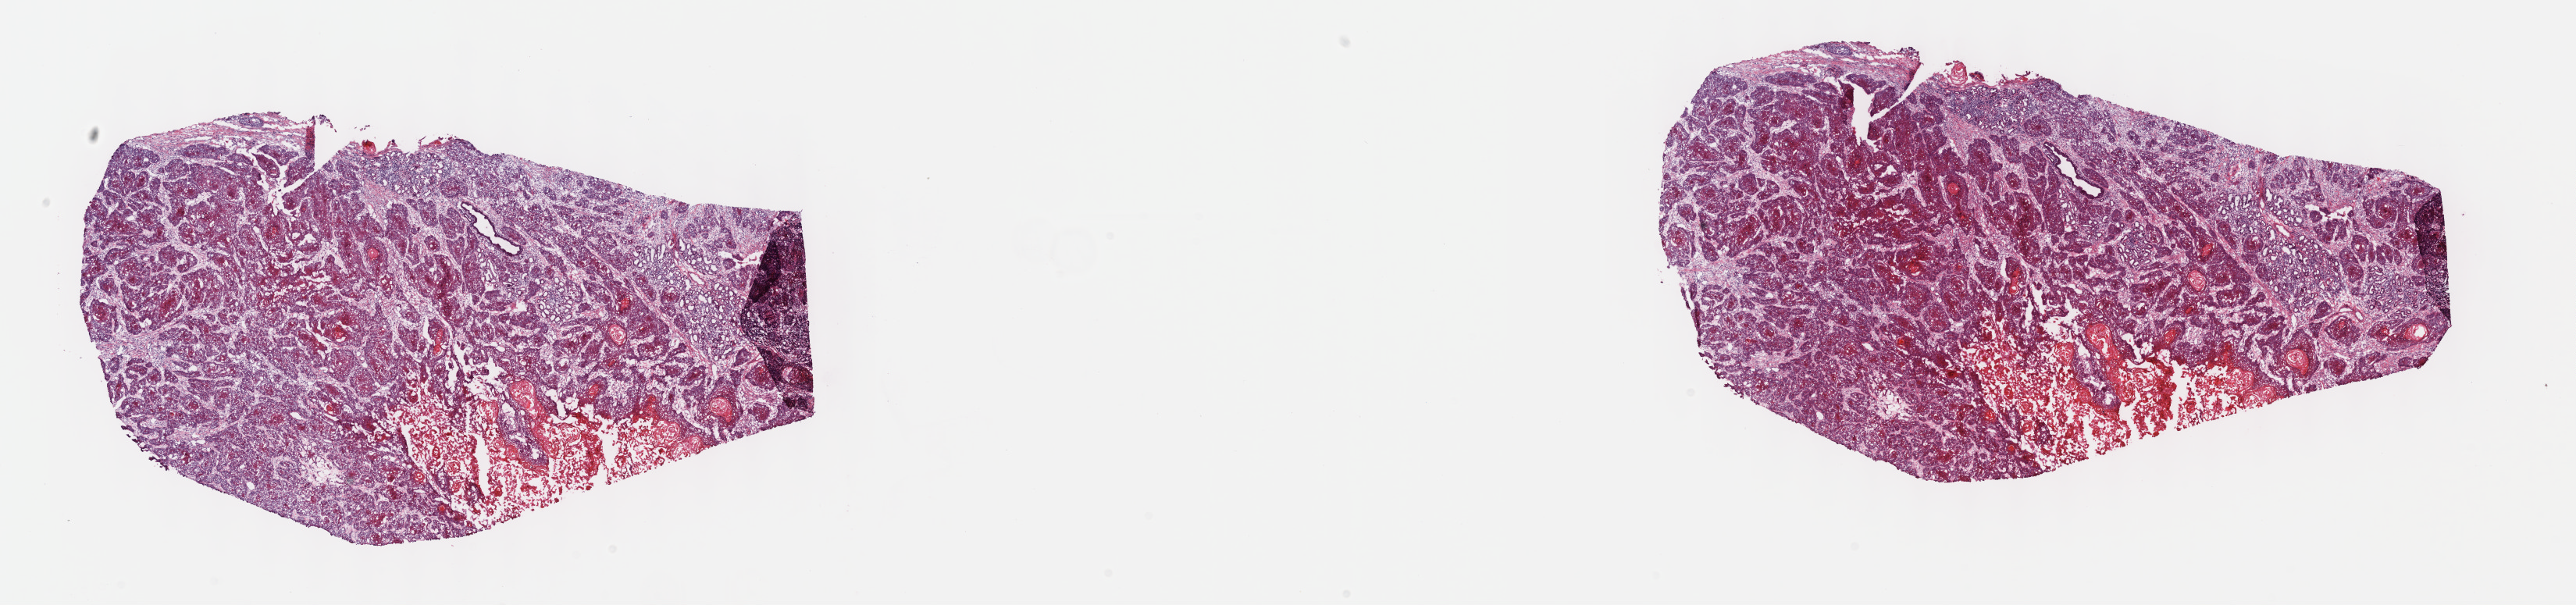
Whole-slide histology image, Hematoxylin and eosin (H&E) stained, whole scanned area (about 26.7 x 6.3 mm) shown as a low-resolution overview, frozen section from the top of the tissue portion, sample: primary tumour, head and neck. Male, age 59 years at initial diagnosis. Histologic grade: G2 (moderately differentiated). Slide review estimates, as recorded: tumour cells 70%, tumour nuclei 80%, normal cells 10%, stromal cells 20%, necrosis 0%. Inflammatory infiltration, as recorded: lymphocyte infiltration 4%, monocyte infiltration 4%, neutrophil infiltration 0%.
- AJCC pathologic stage: IVA
- diagnosis: Squamous cell carcinoma, keratinizing, NOS (larynx, NOS)